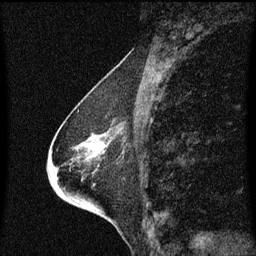
Breast MRI (dynamic contrast-enhanced), one sagittal slice. Slice 28 of 60 in the series (ordered by position). Dynamic contrast-enhanced series, image 2 of 3 at this slice position (ordered by acquisition). 1.5 T. TE 4.2 ms, TR 8.4 ms. 2 mm slice thickness. 256 × 256 image matrix, field of view 200 × 200 mm. Female patient, age 68 years. From the clinical record (not read from this slice): setting: breast cancer imaged before/during neoadjuvant chemotherapy; receptor status: triple-negative.
Outlined on this slice (semi-automatically segmented with operator editing):
- analysis volume of interest (the breast-tissue region the enhancement analysis was run in; not a lesion): bounding box [x1, y1, x2, y2] px = [45, 114, 128, 203]
- tumour enhancement mask (voxels above the 70 % enhancement threshold inside the analysis volume of interest): [89, 144, 102, 157]